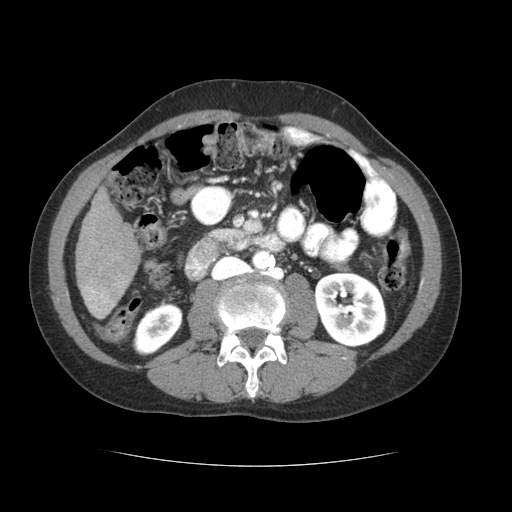
Contrast-enhanced abdominal CT (liver protocol), one axial slice. Slice 15 of 69 in the series (ordered by position). 120 kVp. Soft-tissue window (W 400 / L 40 HU). 2.5 mm slice thickness. 512 × 512 image matrix. From the clinical record (not read from this slice): diagnosis: hepatocellular carcinoma (patient treated with transarterial chemoembolisation; whether this scan precedes or follows treatment is not stated here); TNM stage (as recorded): Stage-II; Child-Pugh class: B; tumour differentiation: poorly differentiated.
Structures marked on this image (semi-automatic segmentation, software-assisted and operator-edited):
- liver parenchyma outside the tumour (the mass and vessels are separate outlines, so this box may not span the whole liver): bounding box [x1, y1, x2, y2] px = [76, 188, 140, 318]
- liver vessels: [86, 287, 114, 312]